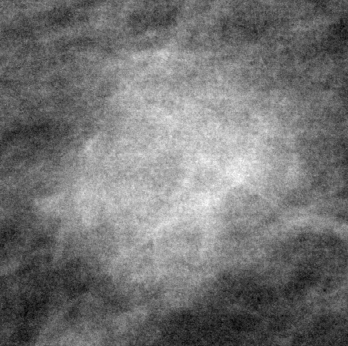
Crop from a digitized film mammogram around one marked abnormality, right breast, MLO view.
Marked abnormality: mass, shape oval, margins ill defined; BI-RADS assessment category 4; pathology (as recorded): benign.